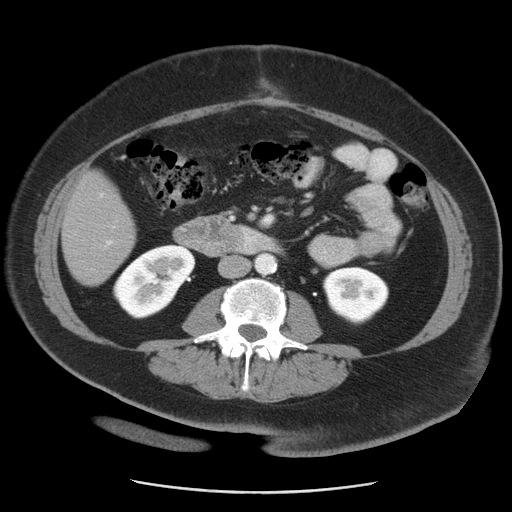
Contrast-enhanced abdominal CT, one axial slice; slice 10 of 55 in the series (ordered by position); 120 kVp; intravenous contrast given; soft-tissue window (W 400 / L 40 HU); 512 × 512 image matrix, field of view 380 × 380 mm. Female patient, age 52 years. From the clinical record (not read from this slice): diagnosis: colorectal cancer liver metastases, imaged before liver resection; multiple liver metastases: yes; largest metastasis: 2.5 cm; disease in both lobes: yes.
Outlined on this slice (outlined manually by an expert reader):
- liver: box from (x=62, y=172) to (x=135, y=285) px
- planned liver remnant (the part of the liver to remain after resection): (x=62, y=196)–(x=131, y=285)
- portal vein (with intrahepatic branches): (x=74, y=192)–(x=118, y=272)